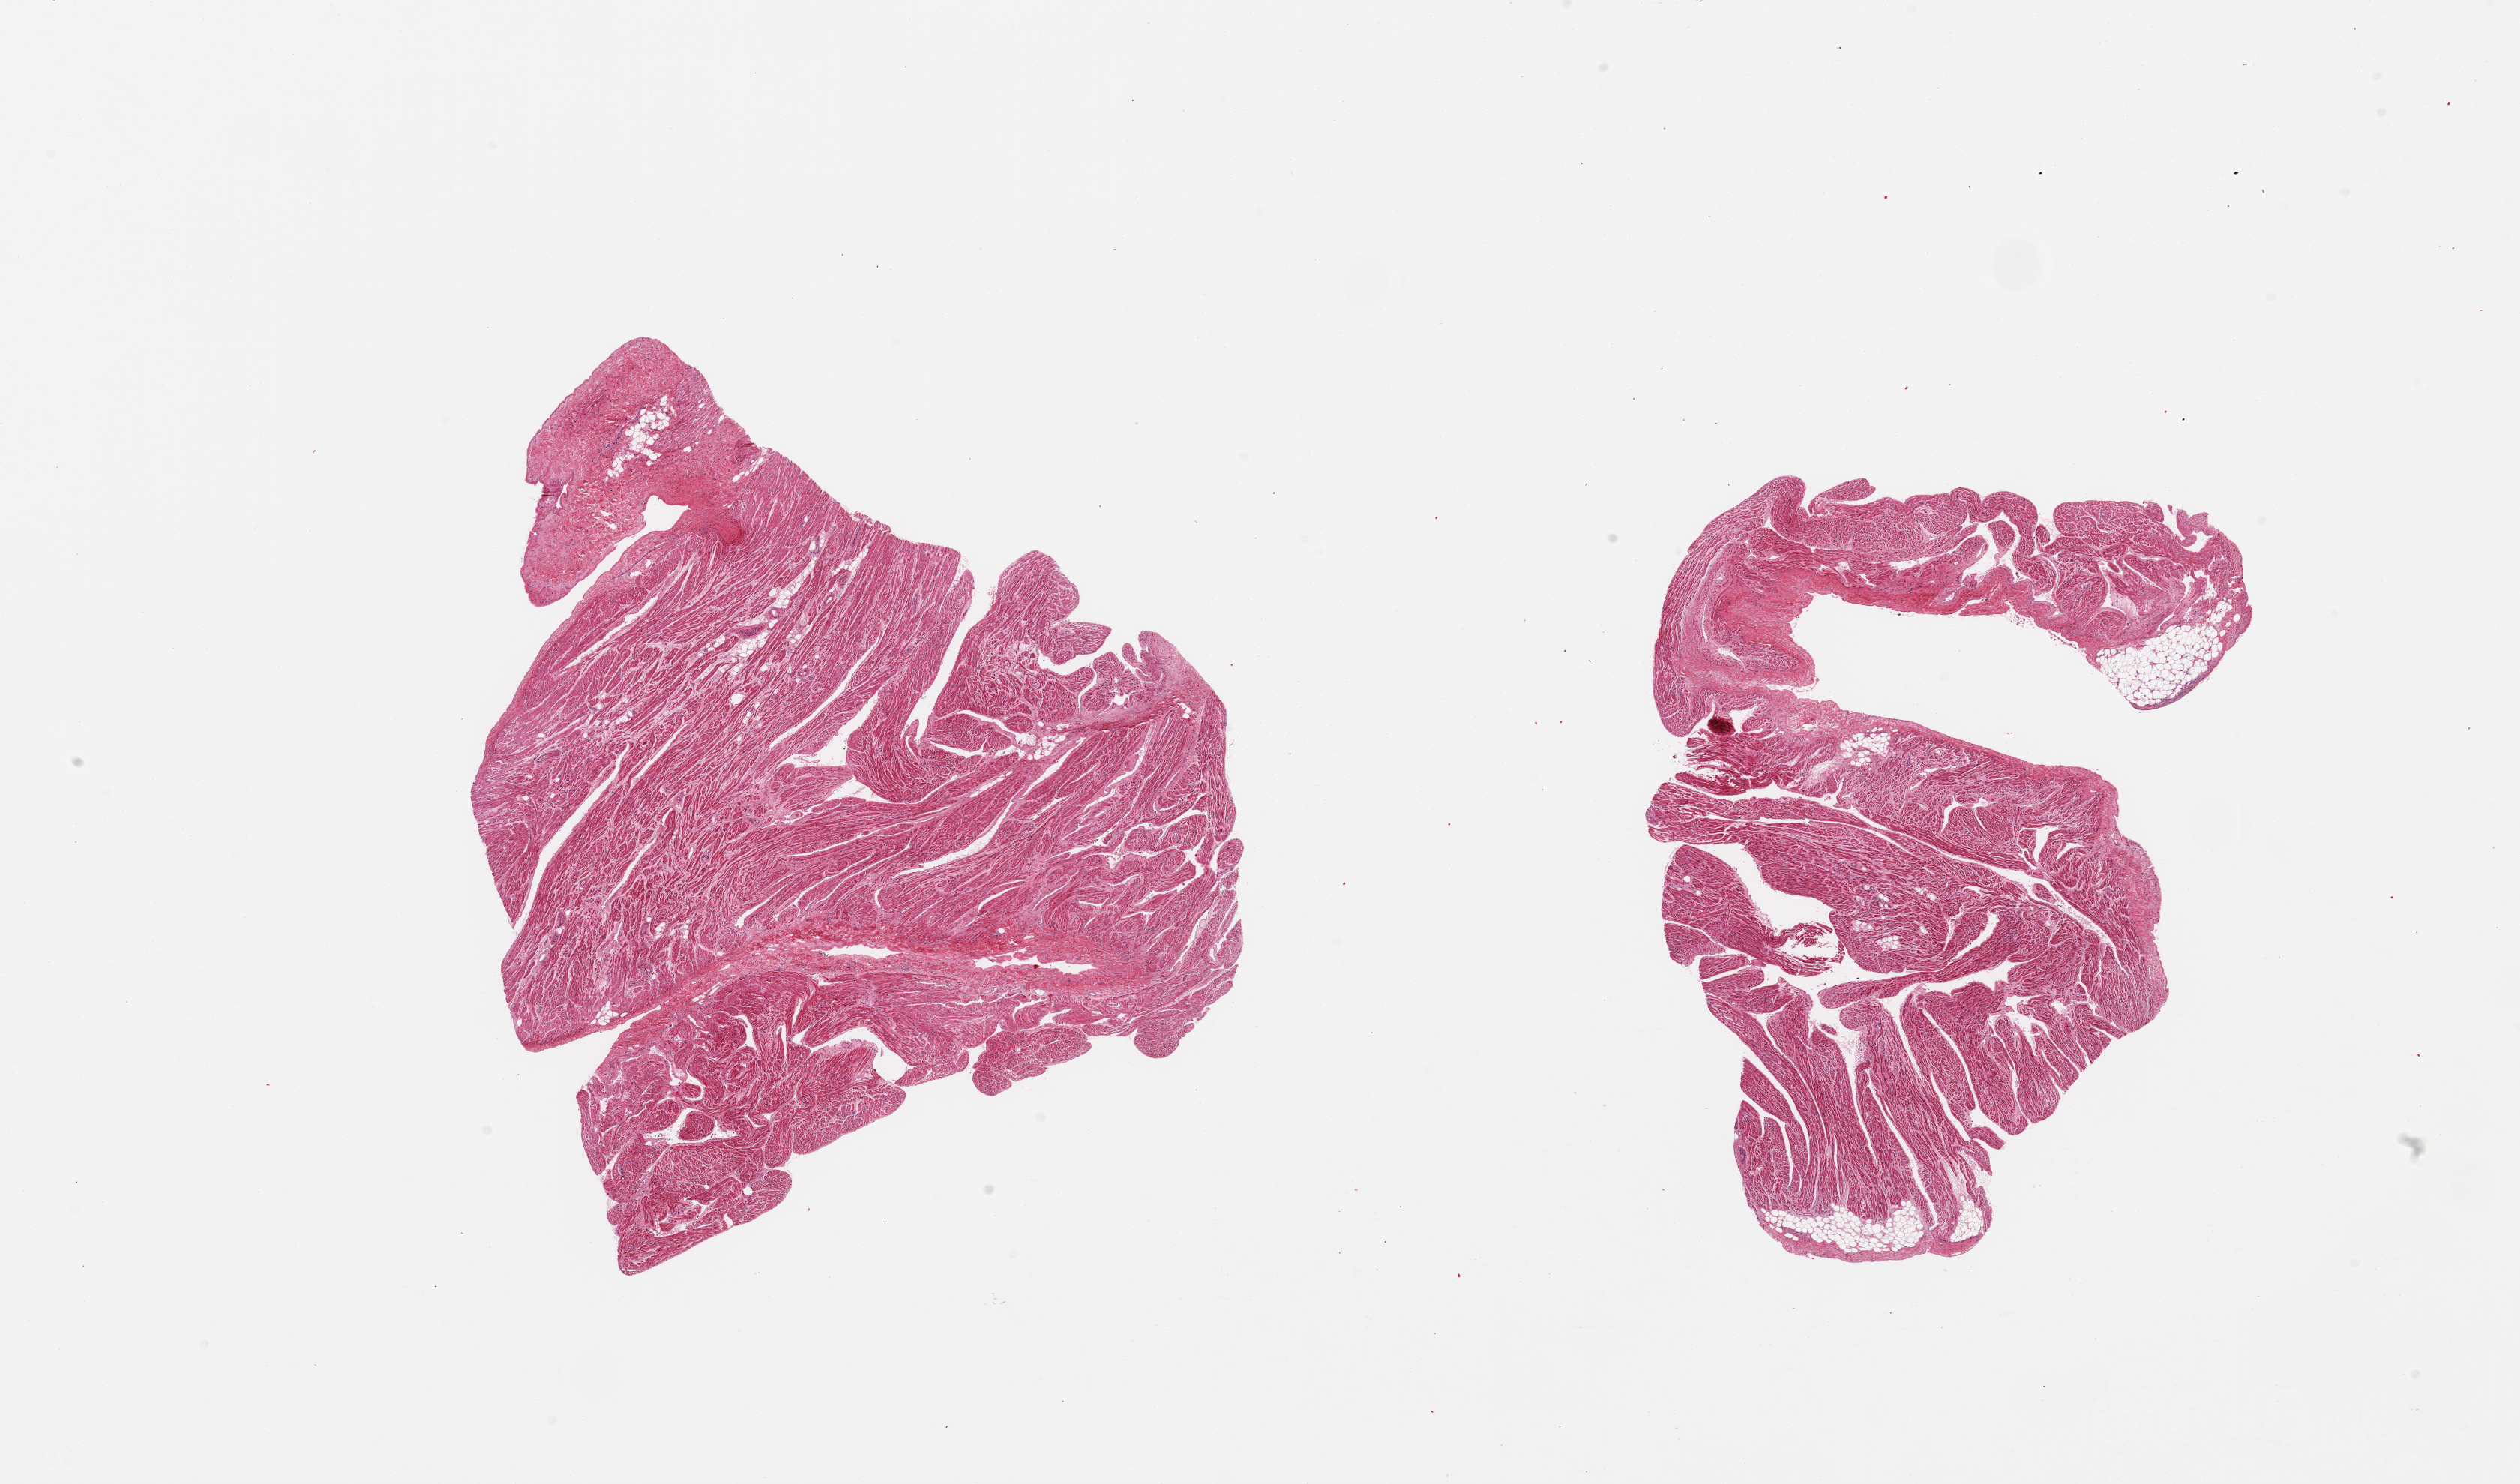
Whole-slide image, H&E stain — whole scanned area (about 26.6 x 15.7 mm) shown as a low-resolution overview, PAXgene-fixed paraffin-embedded (PFPE) section, section of auricular appendage (target tissue), donor tissue sample. Donor: male.
• pathologist's review note for this sample: 2 pieces; includes <10% fat